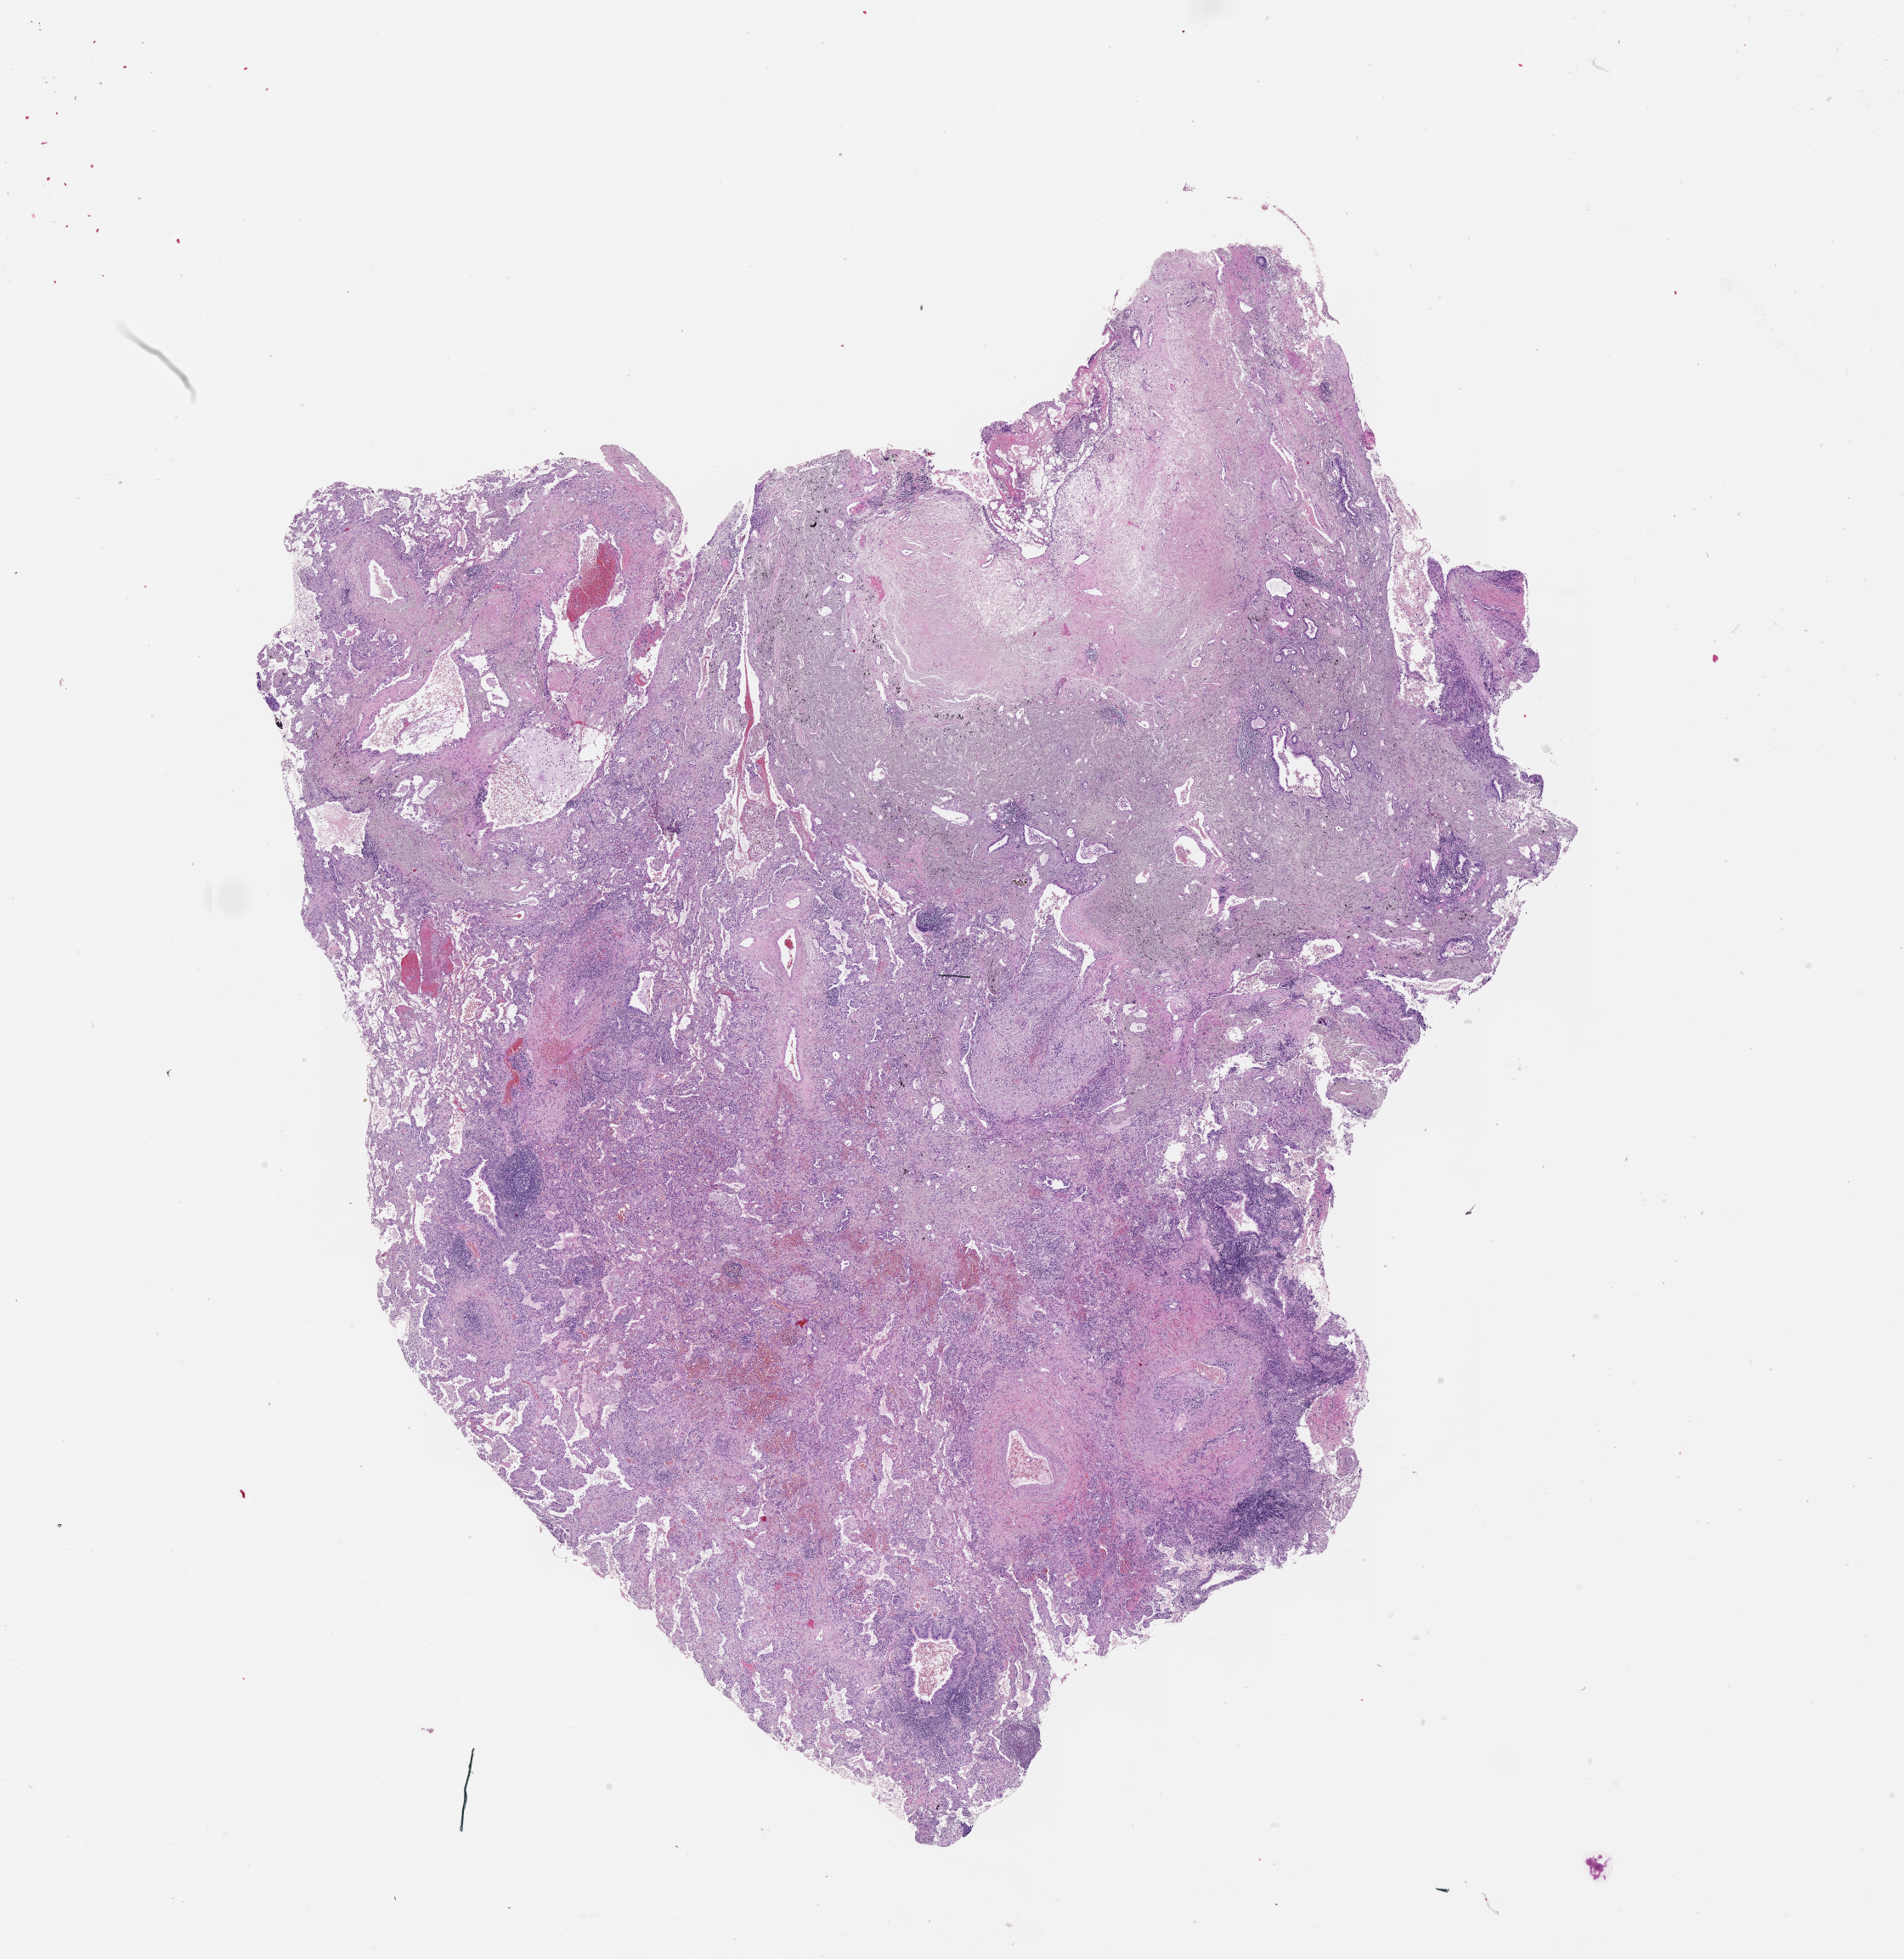
Whole-slide histology image, H&E — low-resolution overview of the scanned area, about 18.0 x 18.6 mm (acquisition: 20x scan), tumour tissue sample, lung. Male, 77 y/o.
Patient diagnosis (cohort enrolment): squamous cell carcinoma (lung).